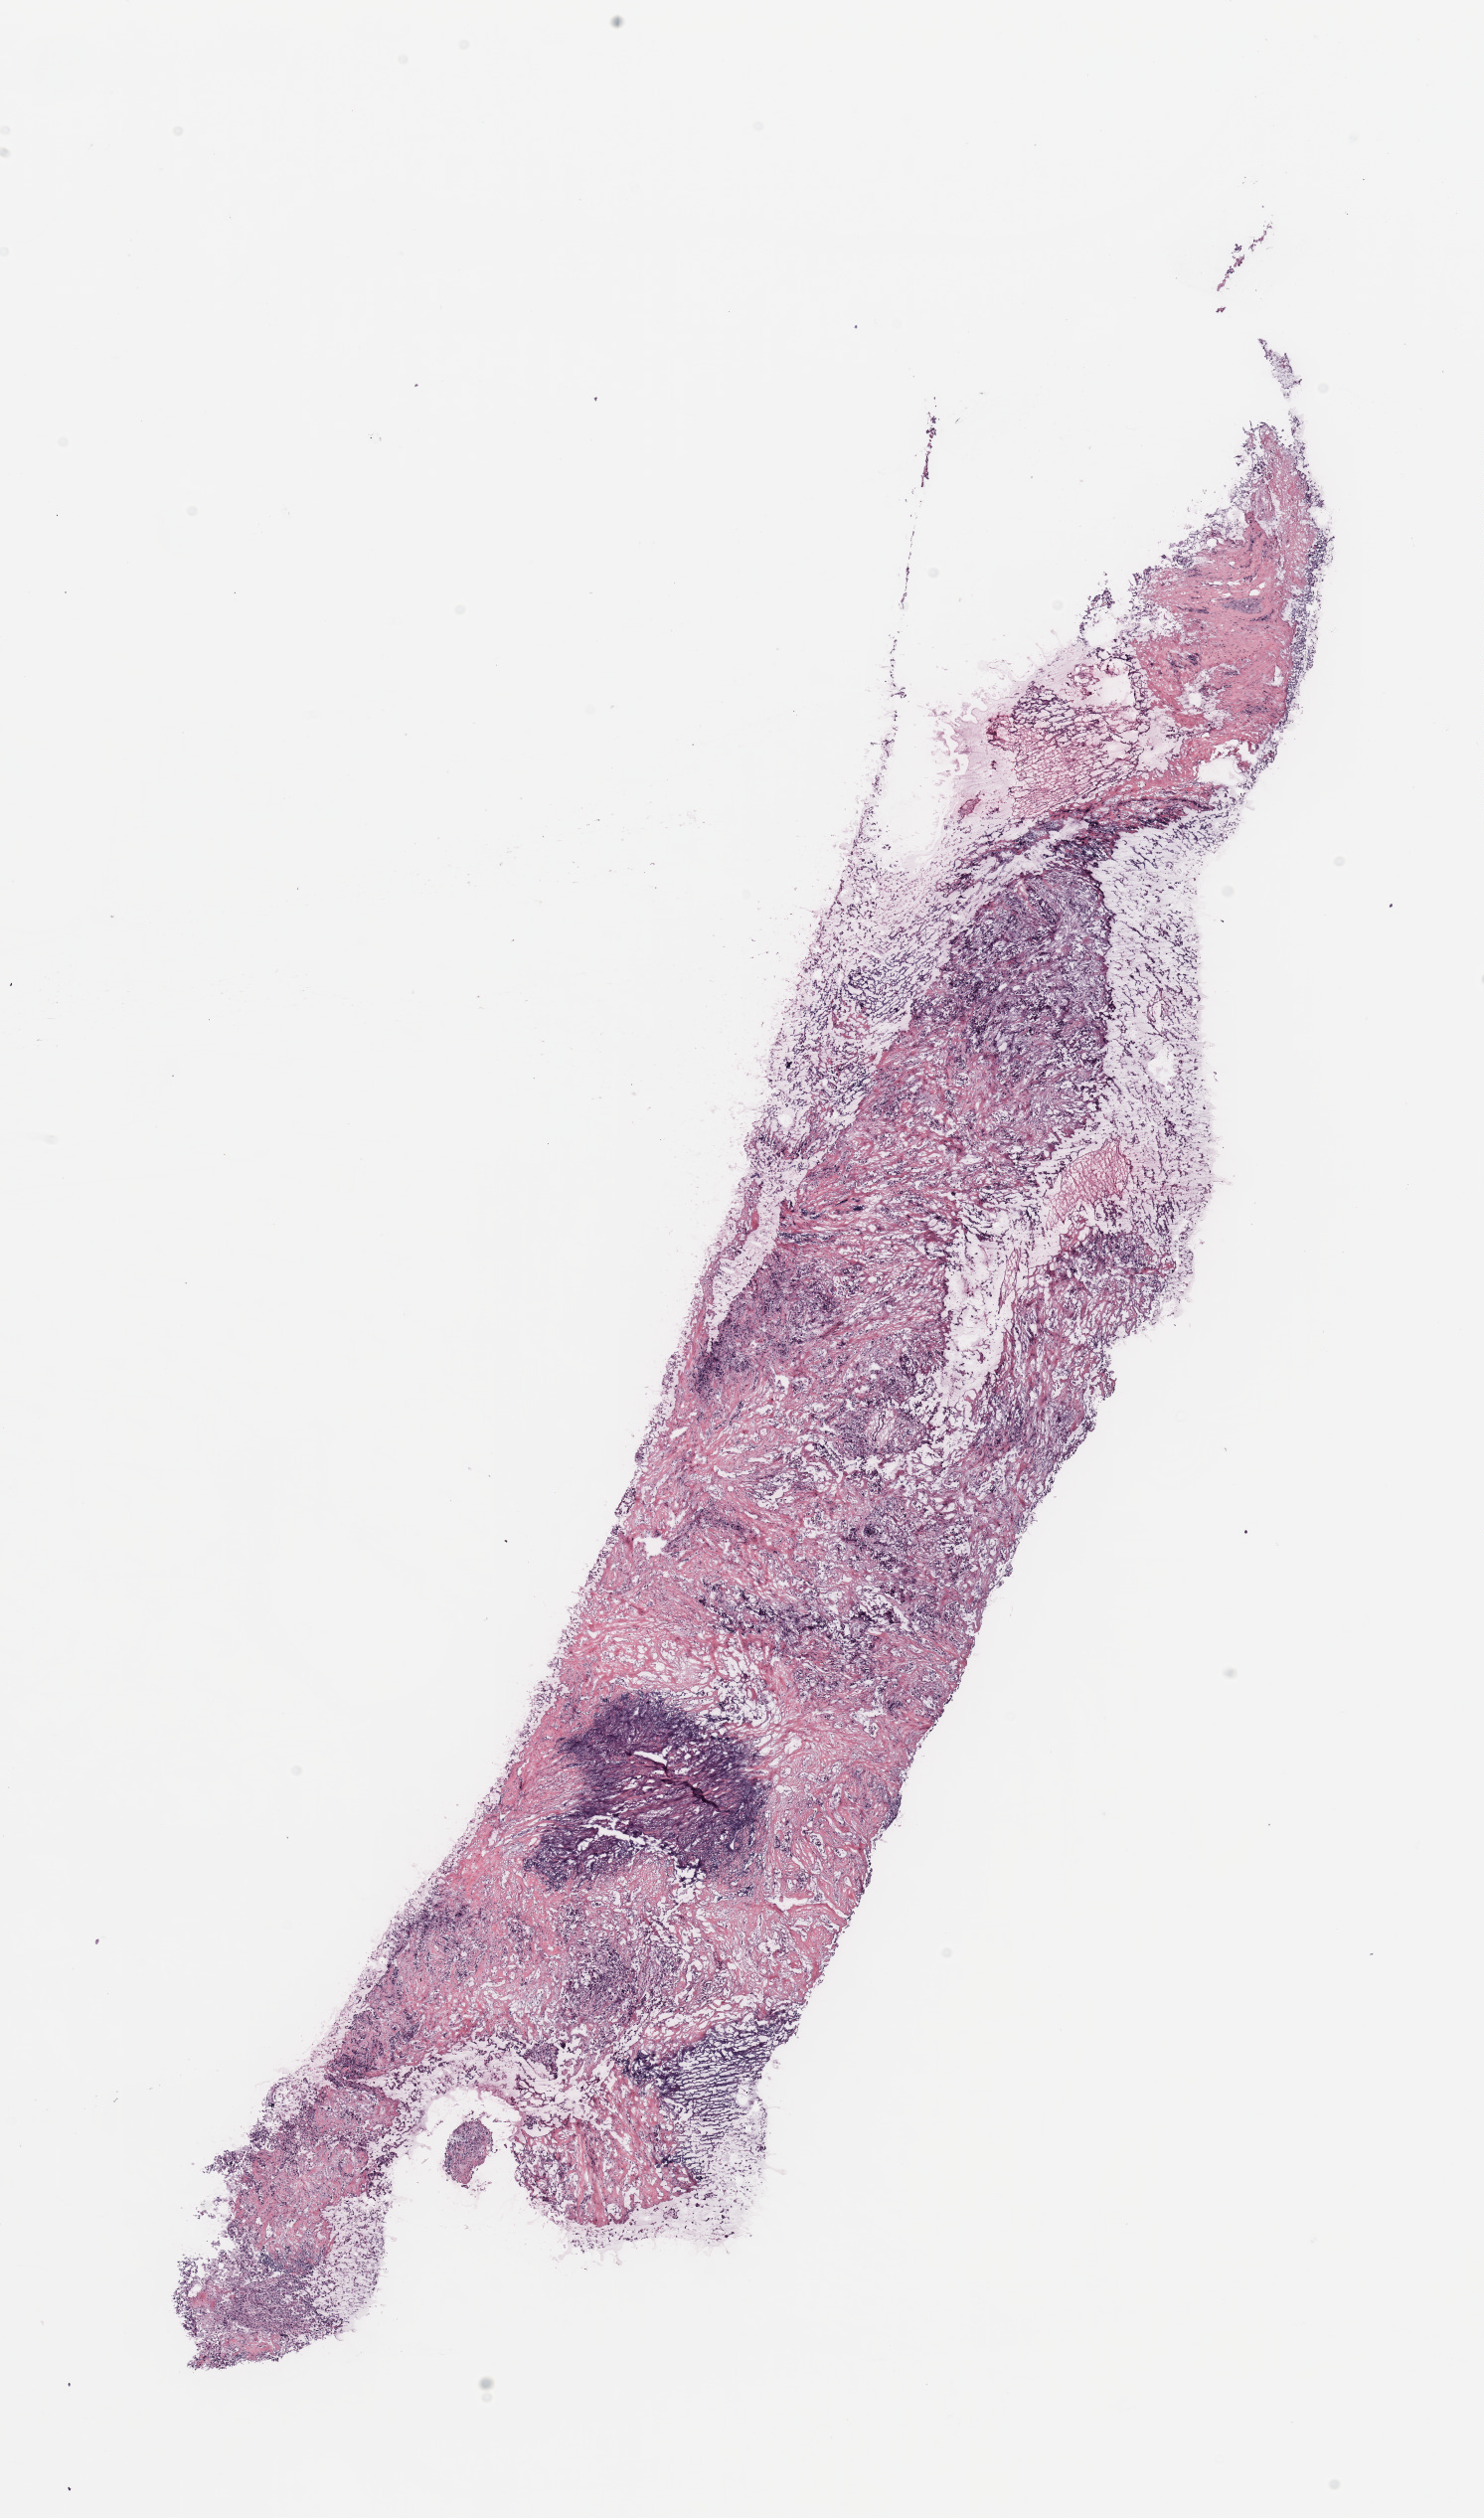
Whole-slide histology image, H&E, a low-resolution overview of the entire scanned area, about 11.8 x 20.0 mm (slide scanned at 20x). Breast, tissue type not recorded.
Patient diagnosis (cohort enrolment): breast cancer (breast).